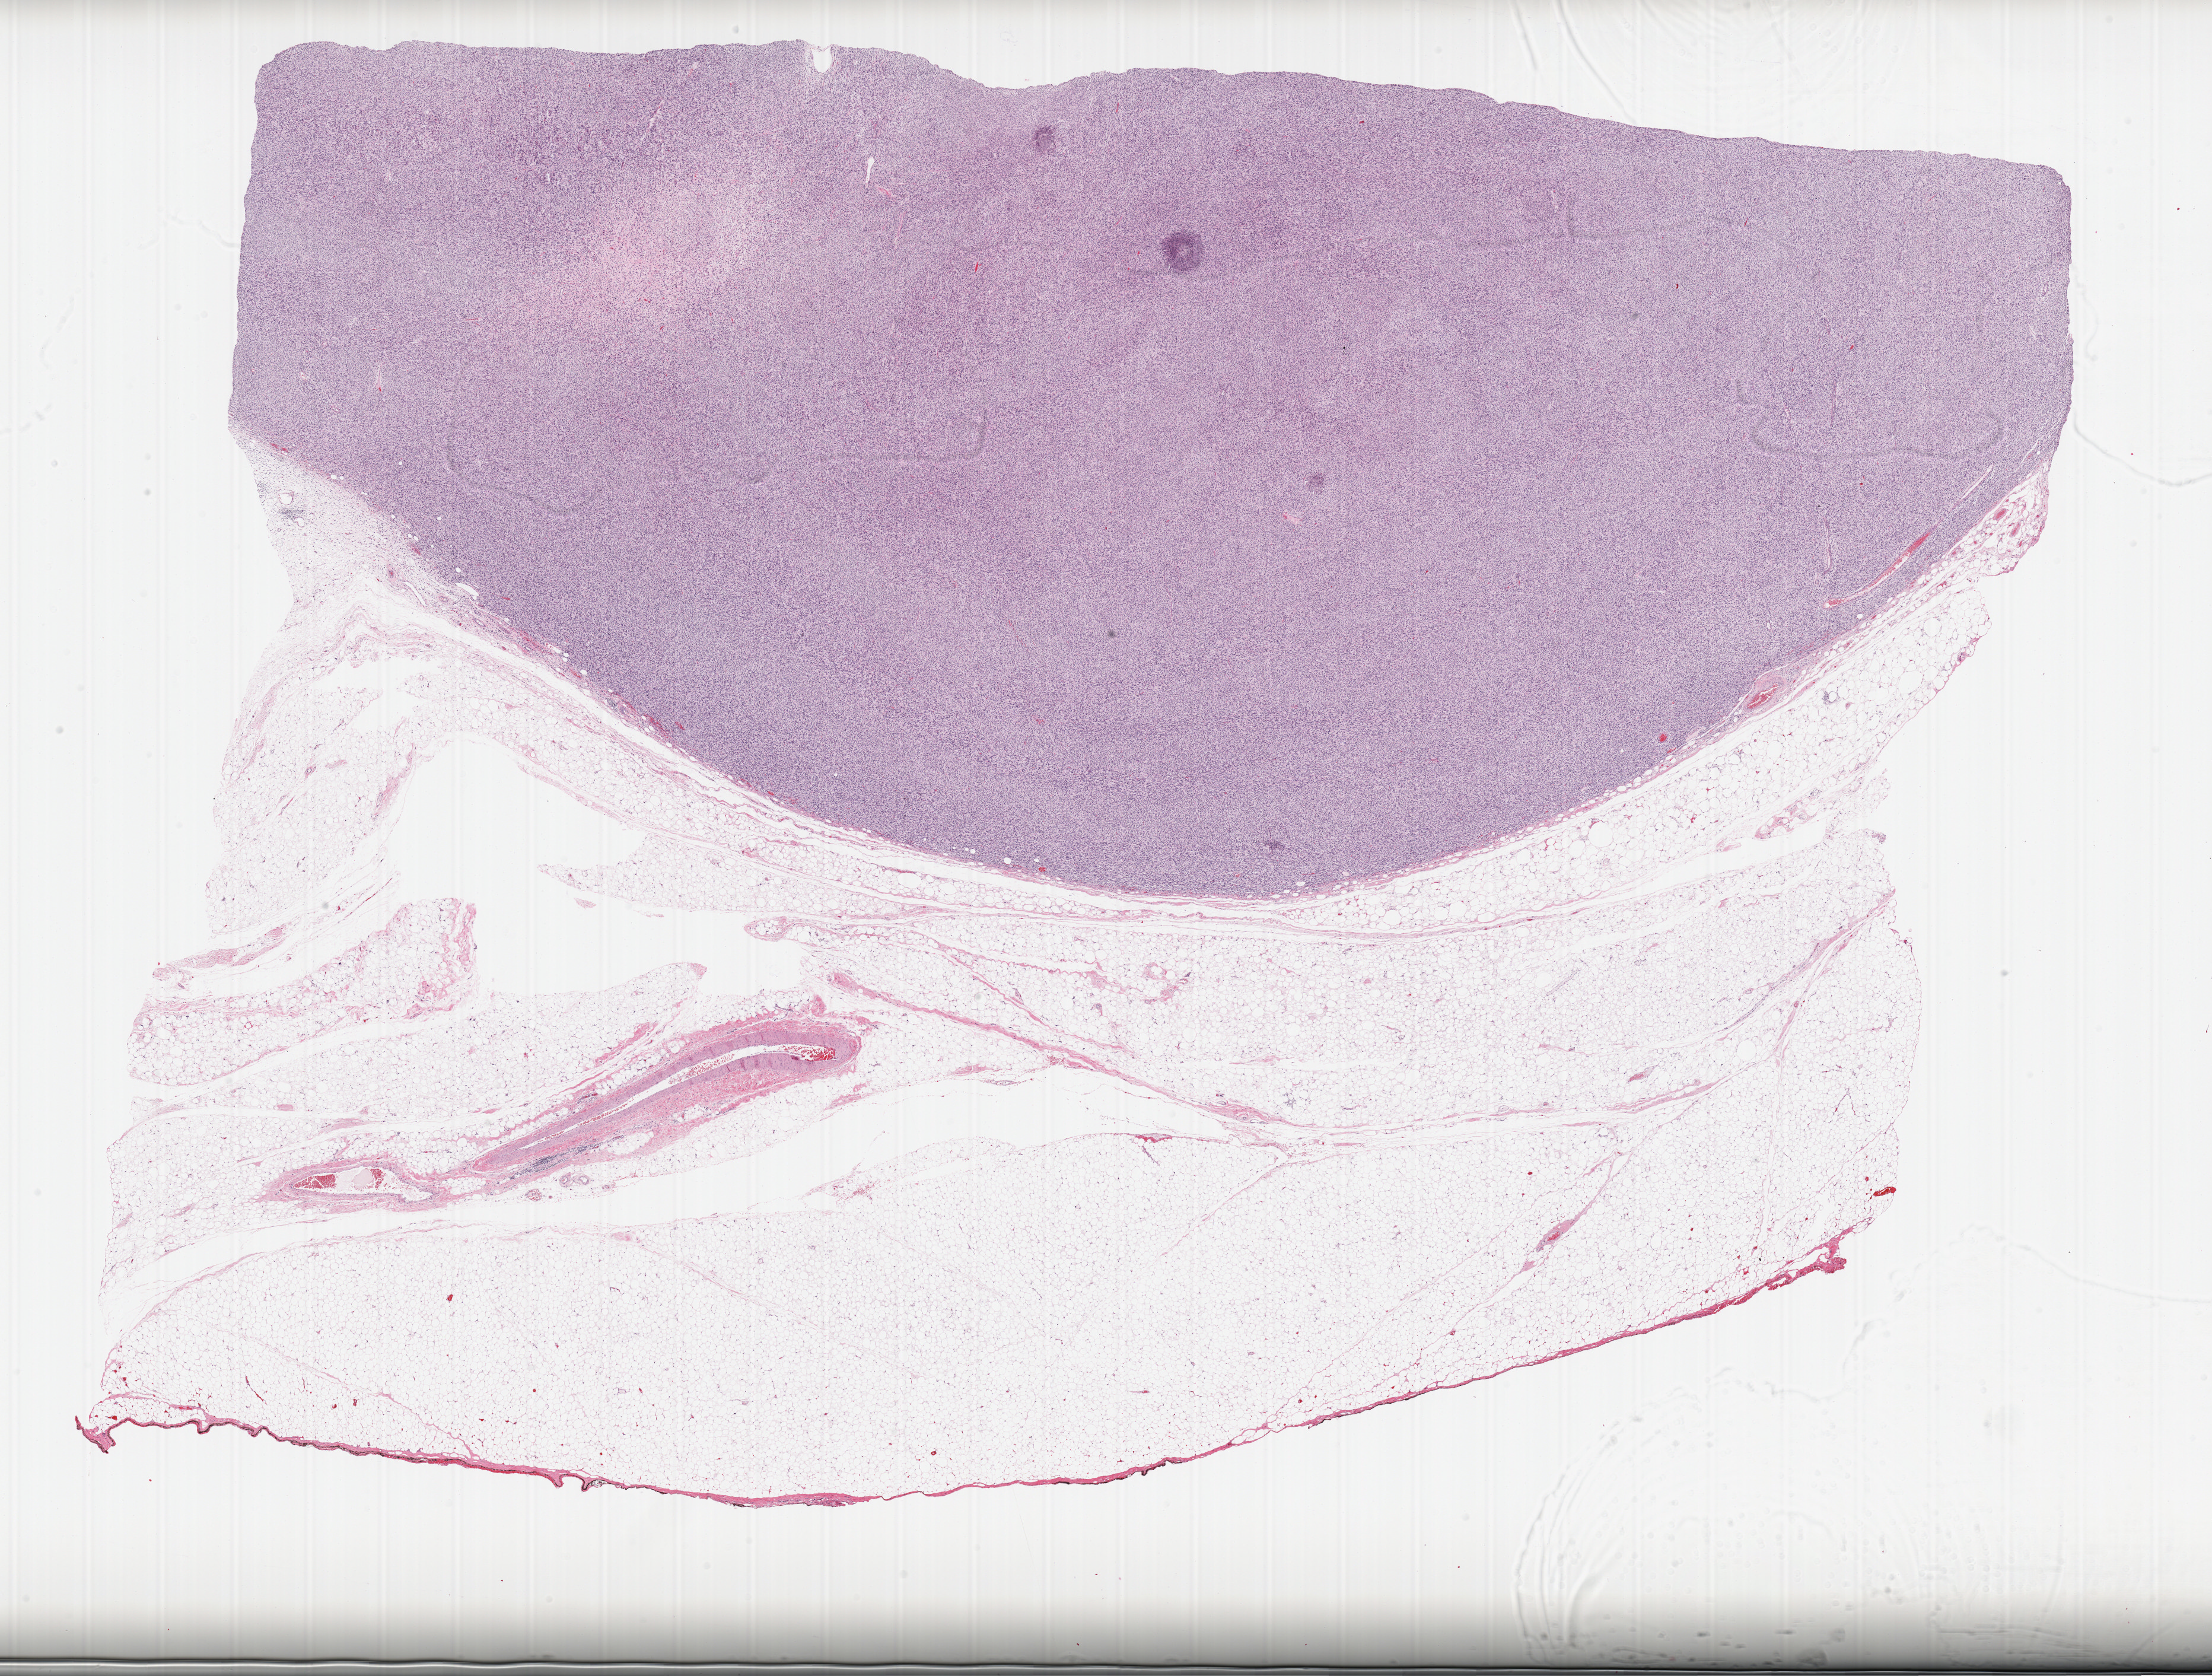
Digitized H&E tissue section (whole slide), a low-resolution overview of the entire scanned area, about 29.7 x 22.5 mm, formalin-fixed paraffin-embedded (FFPE) diagnostic section, primary tumour sample from the retroperitoneum and peritoneum. Female, age 82 years at initial diagnosis.
Diagnosis: Dedifferentiated liposarcoma (retroperitoneum).